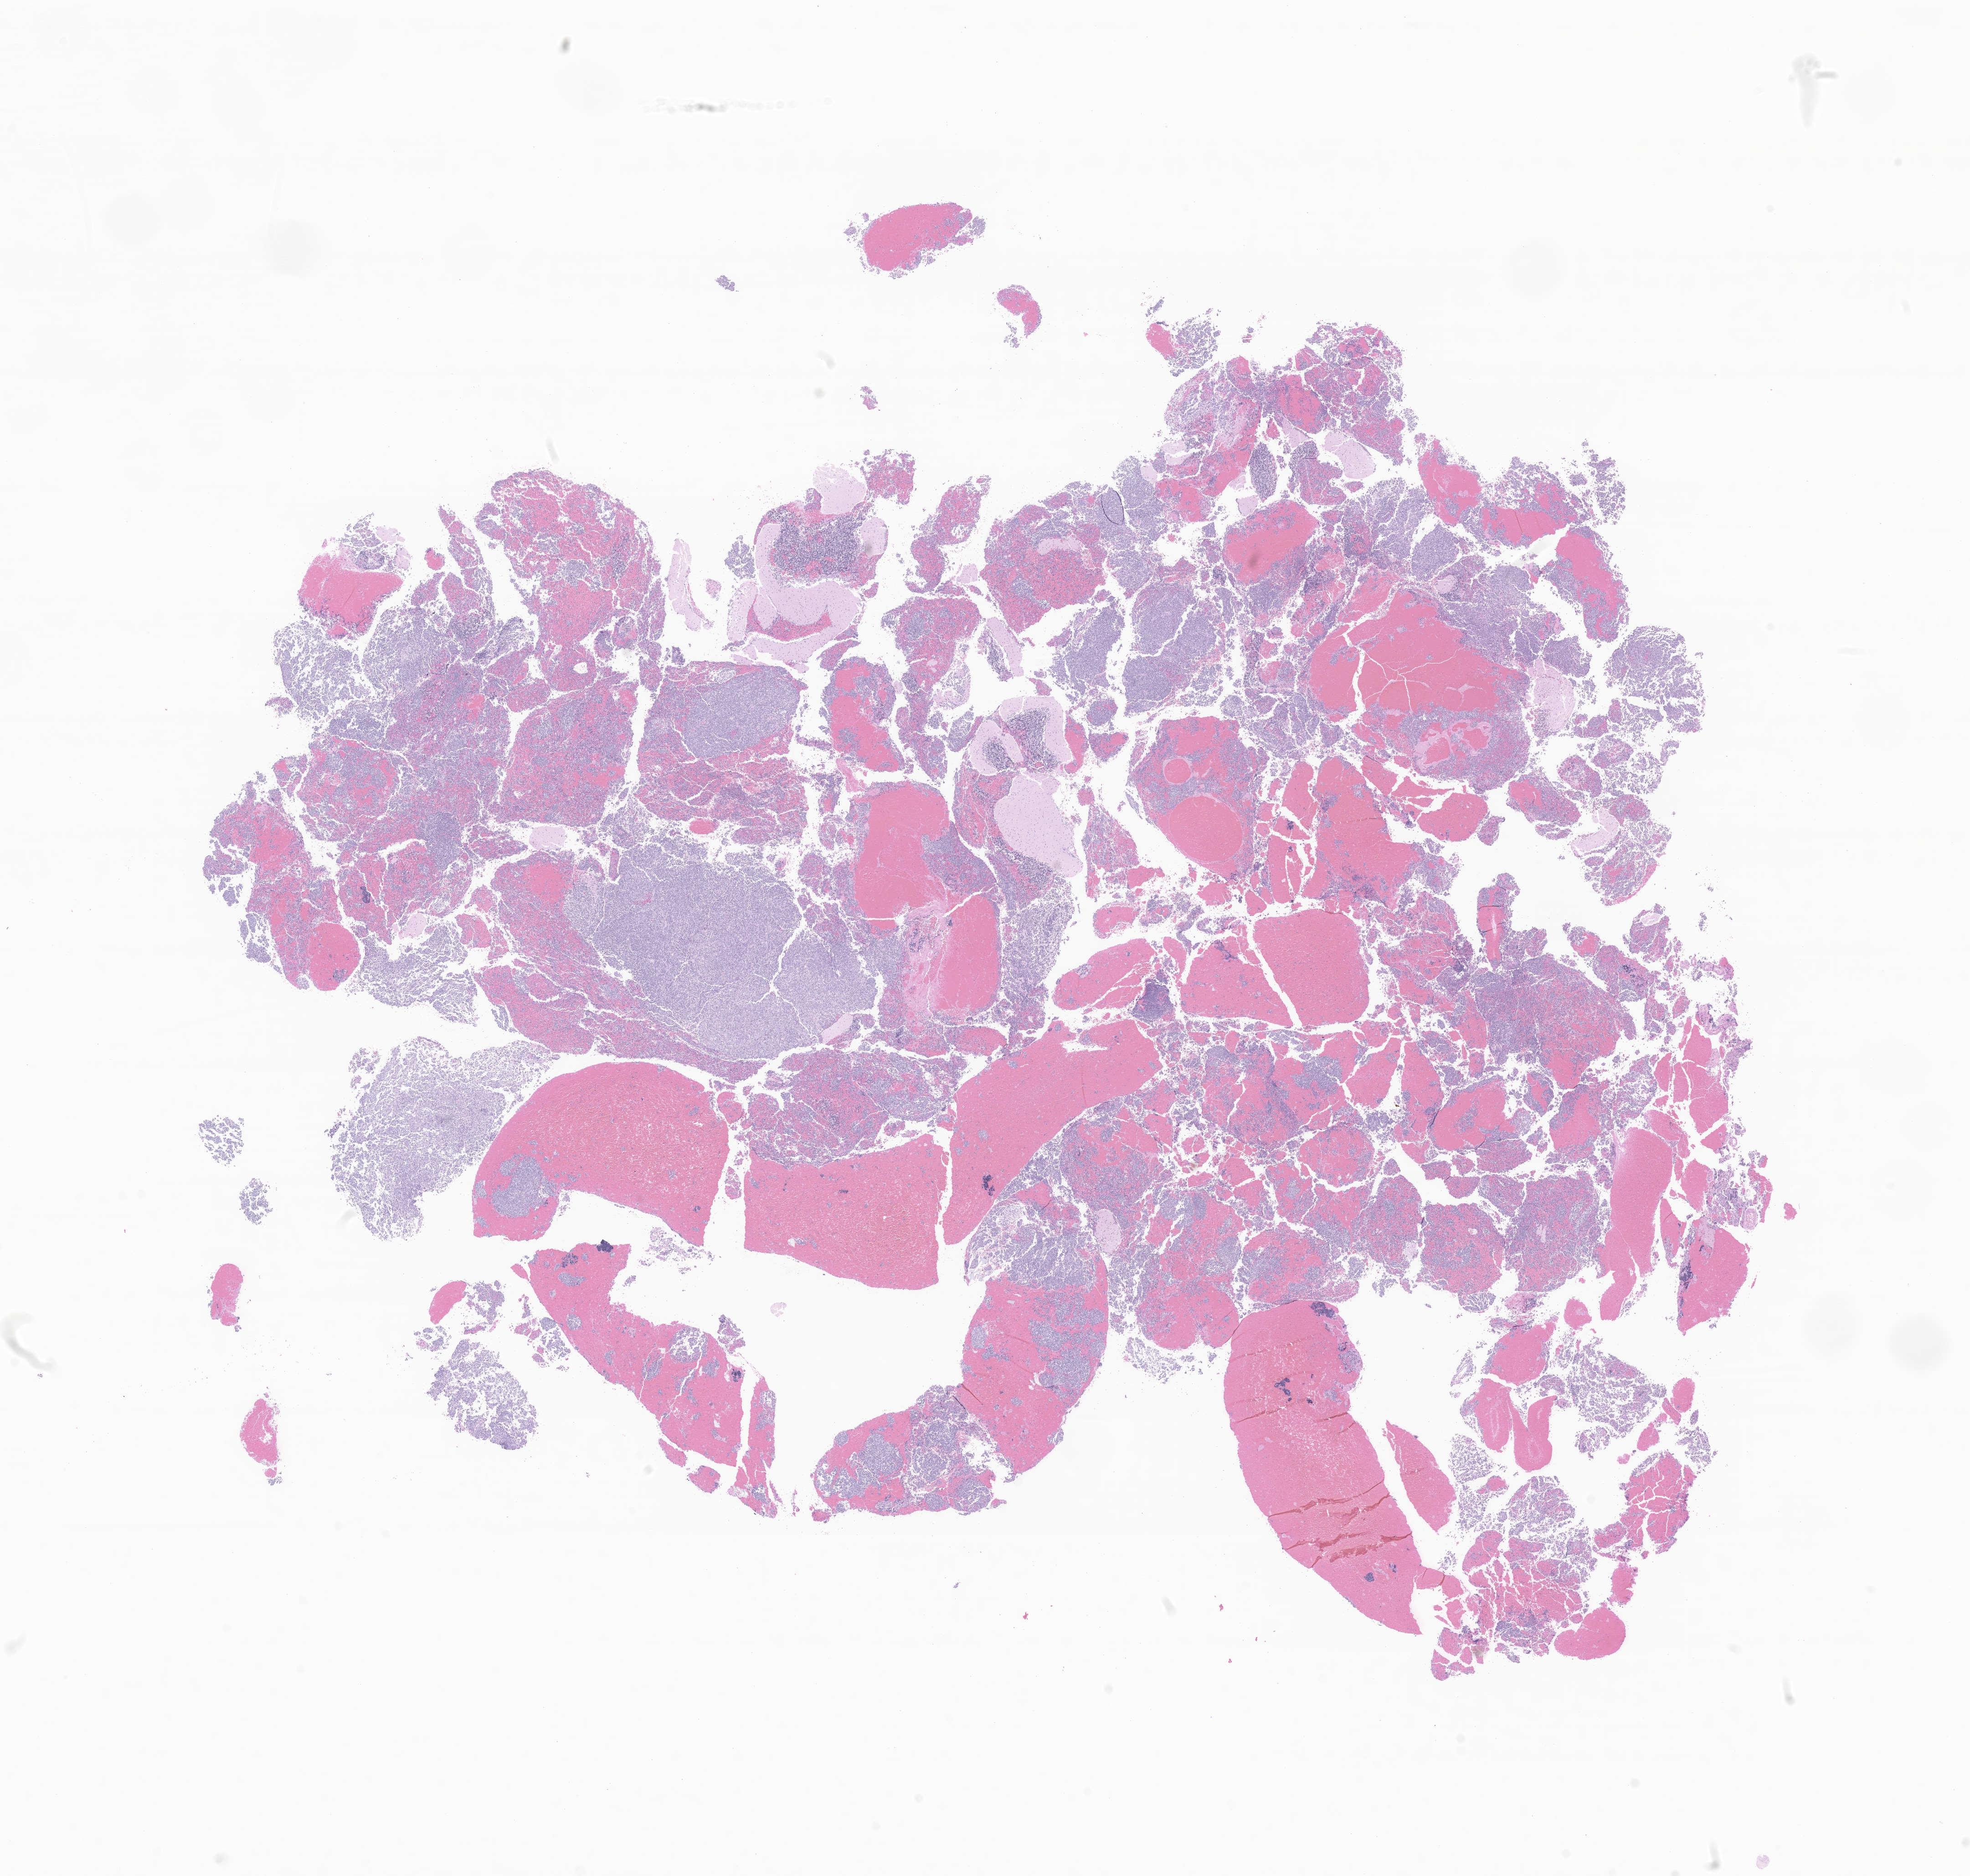
Whole-slide image, haematoxylin and eosin stain of tumor tissue from the brain — low-resolution overview of the scanned area, about 18.2 x 17.4 mm. Formalin-fixed, paraffin-embedded (FFPE) tissue. Patient: male, age 176 days.
- diagnosis: Atypical teratoid/rhabdoid tumor